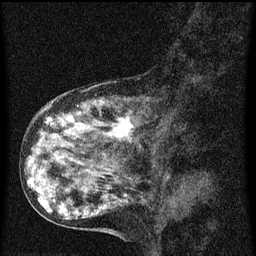
Breast MRI (dynamic contrast-enhanced), one sagittal slice; dynamic contrast-enhanced series, image 2 of 3 at this slice position (ordered by acquisition); 1.5 T; TE 4.2 ms, TR 8 ms; 2 mm slice thickness; 256 × 256 image matrix. Female patient, age 55 years.
Structures marked on this image (semi-automatically segmented with operator editing):
- analysis volume of interest (the breast-tissue region the enhancement analysis was run in; not a lesion): box from (x=38, y=92) to (x=157, y=159) px
- tumour enhancement mask (voxels above the 70 % enhancement threshold inside the analysis volume of interest): (x=46, y=116)–(x=135, y=143)